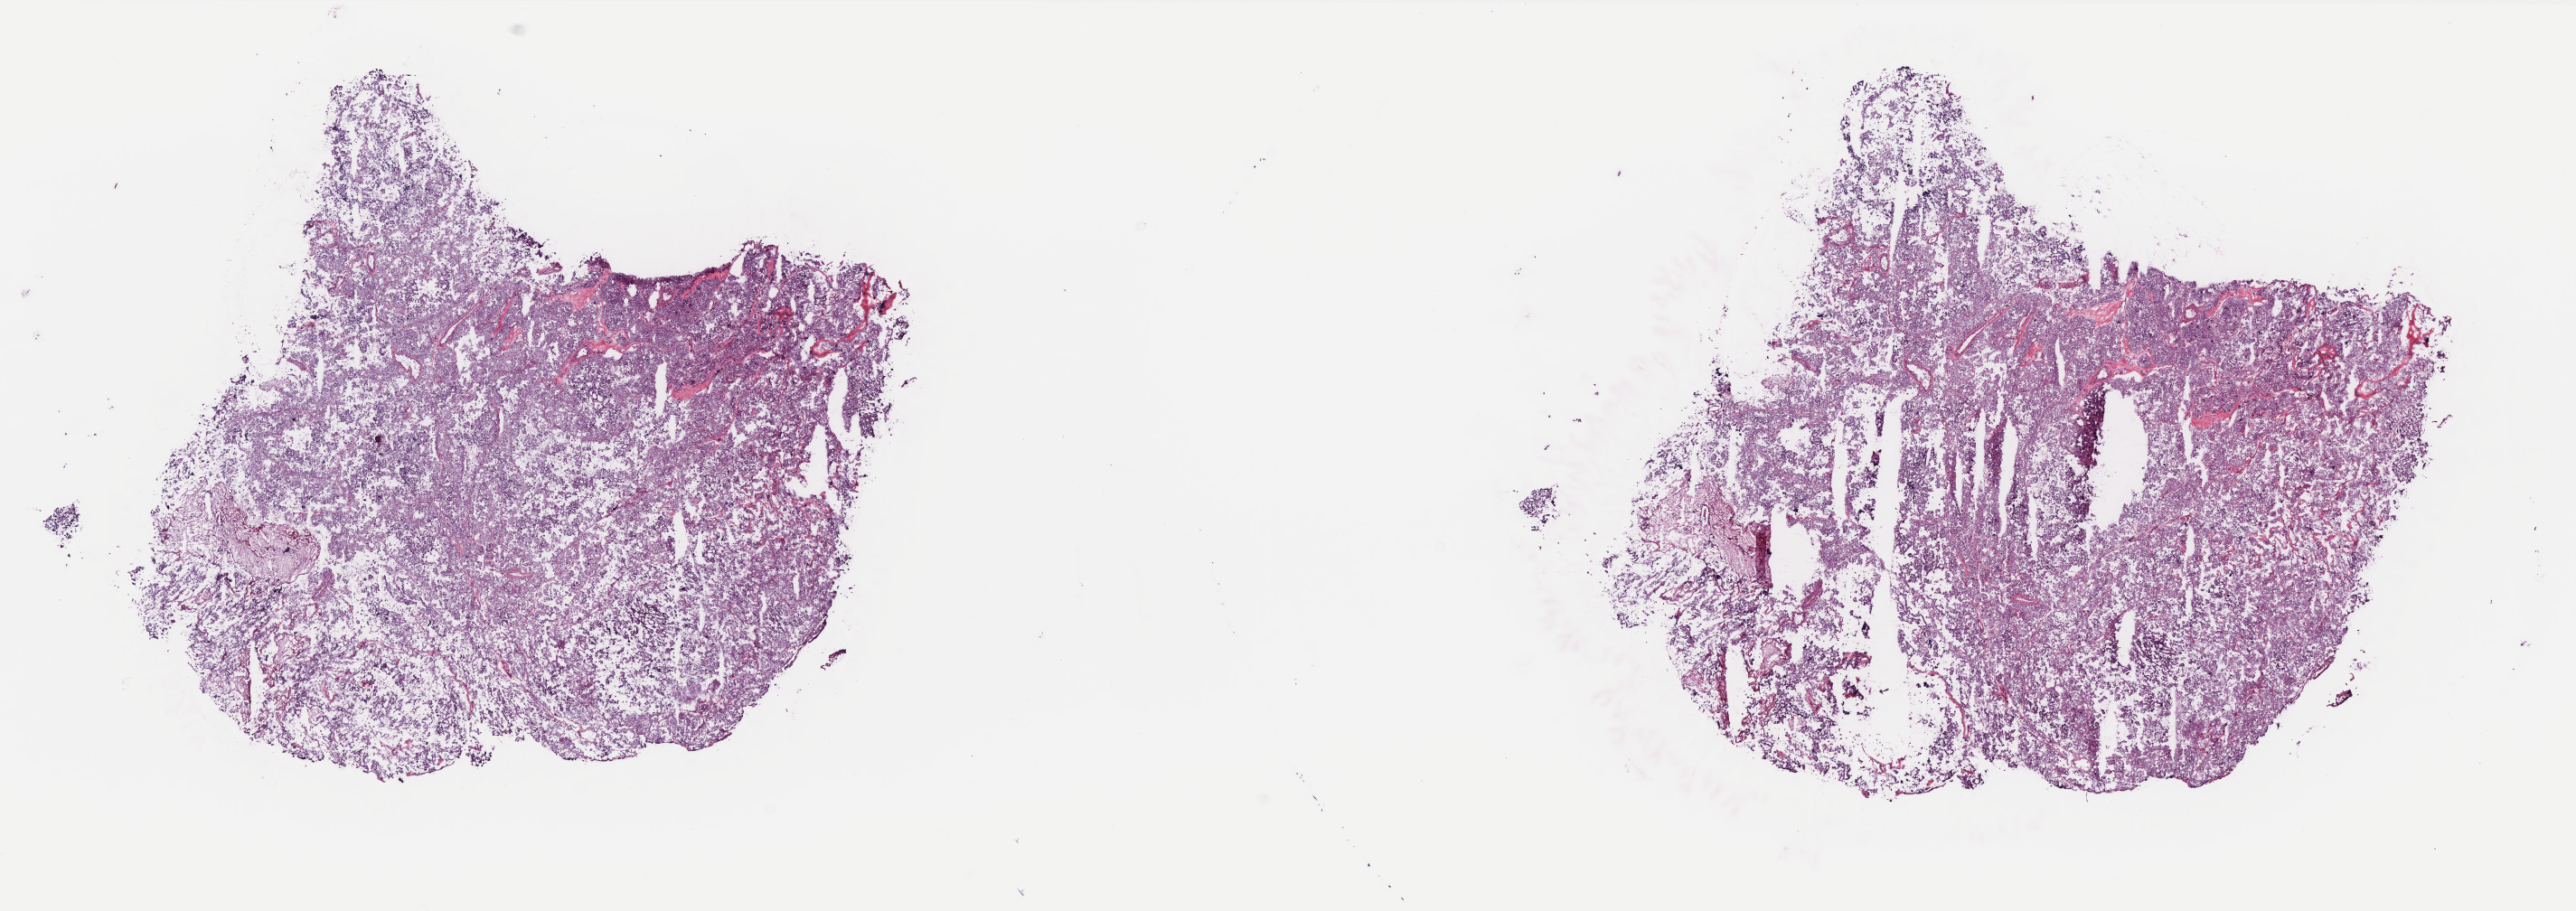
Hematoxylin and eosin (H&E) stained whole-slide image — whole scanned area (about 22.8 x 8.1 mm, from a 40x scan) shown as a low-resolution overview. Frozen section. Sample: primary tumour, kidney. Patient: male, age at initial diagnosis 56 years. Slide review estimates, as recorded: tumour cells 90%, tumour nuclei 95%.
Pathologic diagnosis: Renal cell carcinoma, chromophobe type.